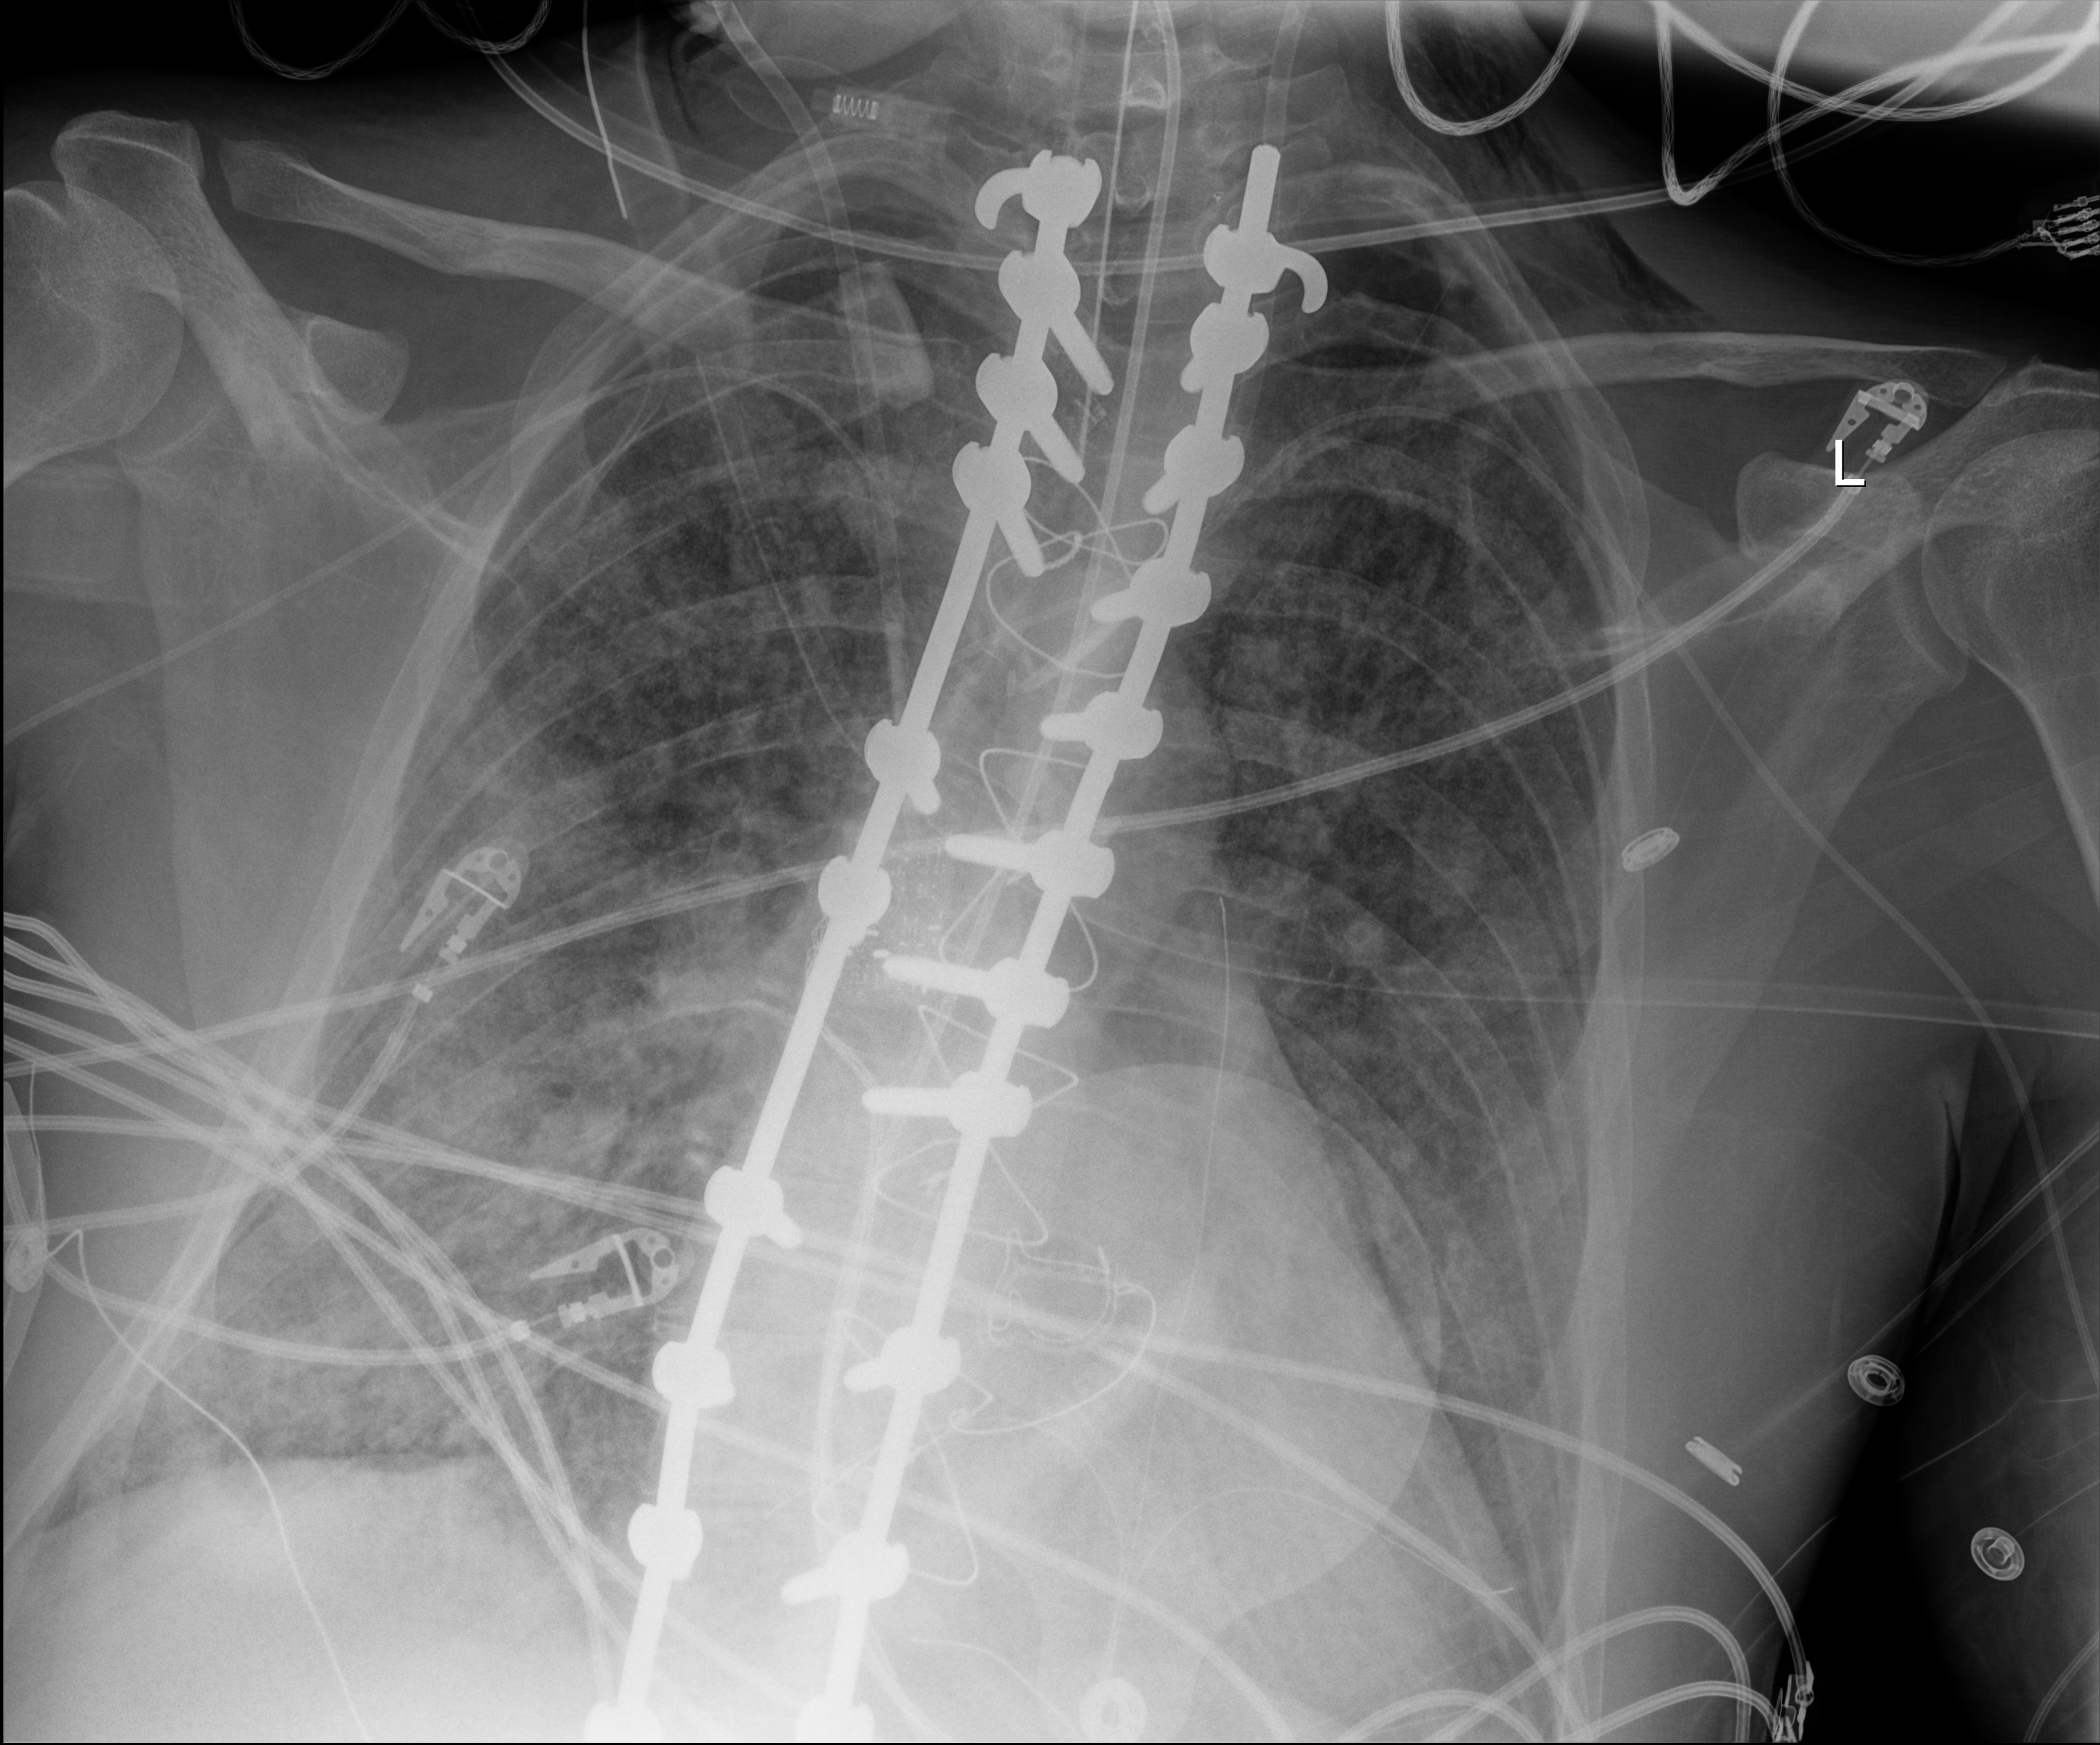
Chest X-ray (portable), anteroposterior (AP) projection. Adult patient hospitalised with COVID-19, age 18–59 years.
From the hospital-stay record, not from the radiograph (when in the stay this image was taken is not recorded):
- hypertension (admission record): no